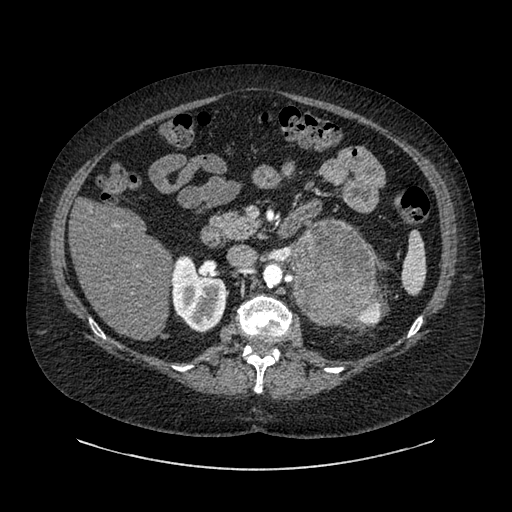
Contrast-enhanced abdominal CT, one axial slice. Slice 533 of 769 in the series (ordered by position). Reconstruction kernel SOFT. 120 kVp. Intravenous contrast given. Soft-tissue window (W 400 / L 40 HU). 0.62 mm slice thickness. 512 × 512 image matrix, field of view 460 × 460 mm. Patient: female, 61 years. From the clinical record (not read from this slice): diagnosis: adrenocortical carcinoma; tumour side: left adrenal; tumour size at pathology: 13 cm; Ki-67 index: 79 %; stage (as recorded): 2.
Annotated regions visible in this slice (semi-automatic segmentation, software-assisted and operator-edited):
- mass: bounding box [x1, y1, x2, y2] px = [293, 222, 372, 324]